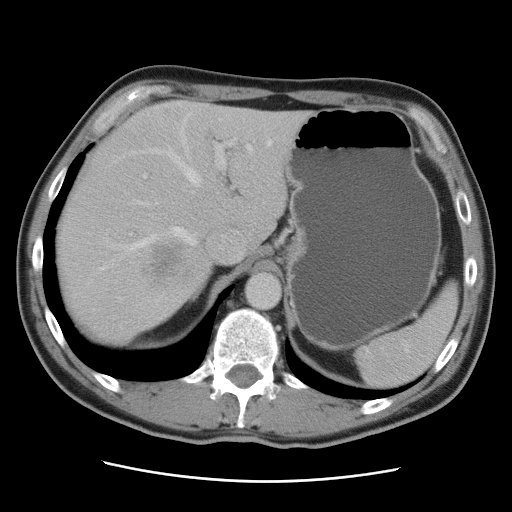
Contrast-enhanced abdominal CT, one axial slice. 120 kVp. Intravenous contrast given. Soft-tissue window (W 400 / L 40 HU). 5 mm slice thickness. 512 × 512 image matrix, field of view 366 × 366 mm. Male patient, age 59 years. Case-level facts recorded for this patient, not image findings: diagnosis: colorectal cancer liver metastases, imaged before liver resection; multiple liver metastases: yes; largest metastasis: 0.6 cm.
Structures marked on this image (outlined manually by an expert reader):
- hepatic veins: bounding box [x1, y1, x2, y2] px = [98, 123, 272, 272]
- liver: [56, 100, 309, 346]
- planned liver remnant (the part of the liver to remain after resection): [101, 100, 307, 249]
- portal vein (with intrahepatic branches): [143, 139, 236, 178]
- liver metastasis: [151, 247, 183, 278]